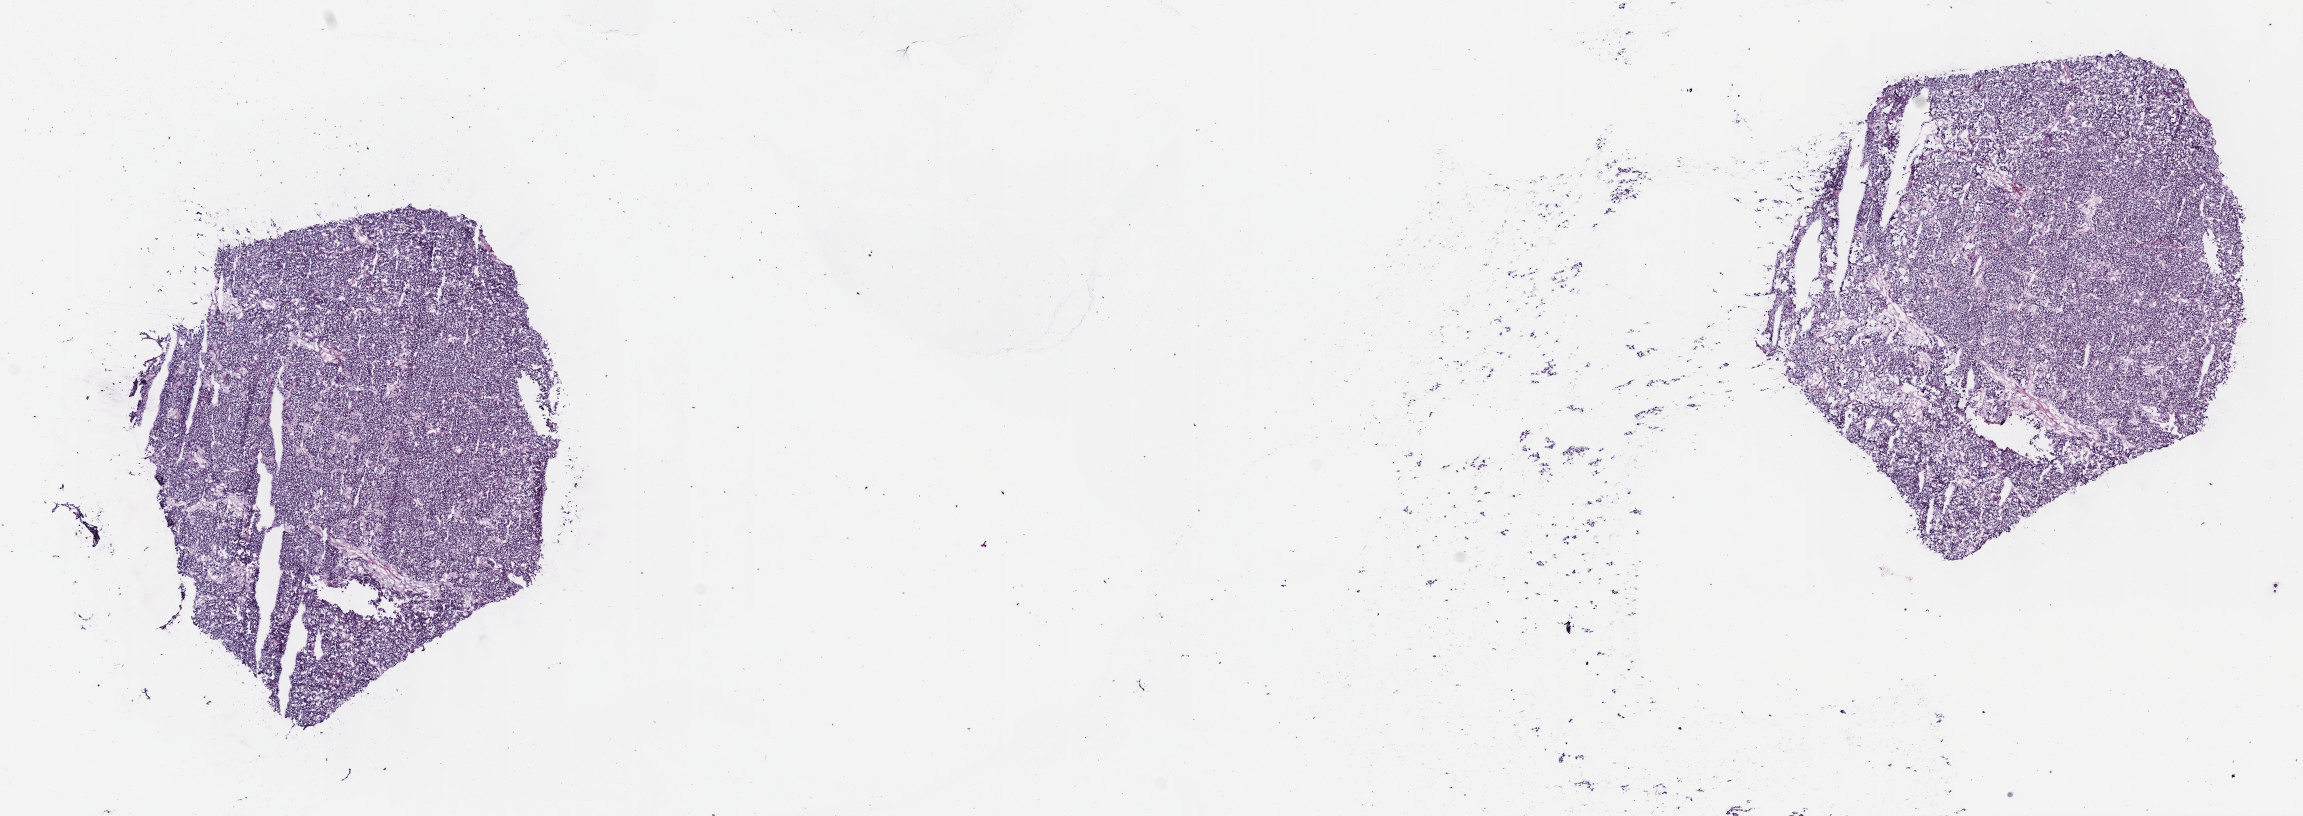
H&E-stained whole-slide image — whole scanned area (about 18.6 x 6.6 mm) shown as a low-resolution overview; frozen section from the top of the tissue portion; adrenal gland, primary tumour sample. Male, age 66 years at initial diagnosis. Composition of this section per pathologist review: tumour cells 80%, tumour nuclei 80%, normal cells 0%, stromal cells 10%, necrosis 10%. Inflammatory infiltration, as recorded: lymphocyte infiltration 40%, monocyte infiltration 20%, neutrophil infiltration 20%.
Pathologic diagnosis: Pheochromocytoma, malignant. Lymph nodes positive (case pathology): 0 of 4 examined.